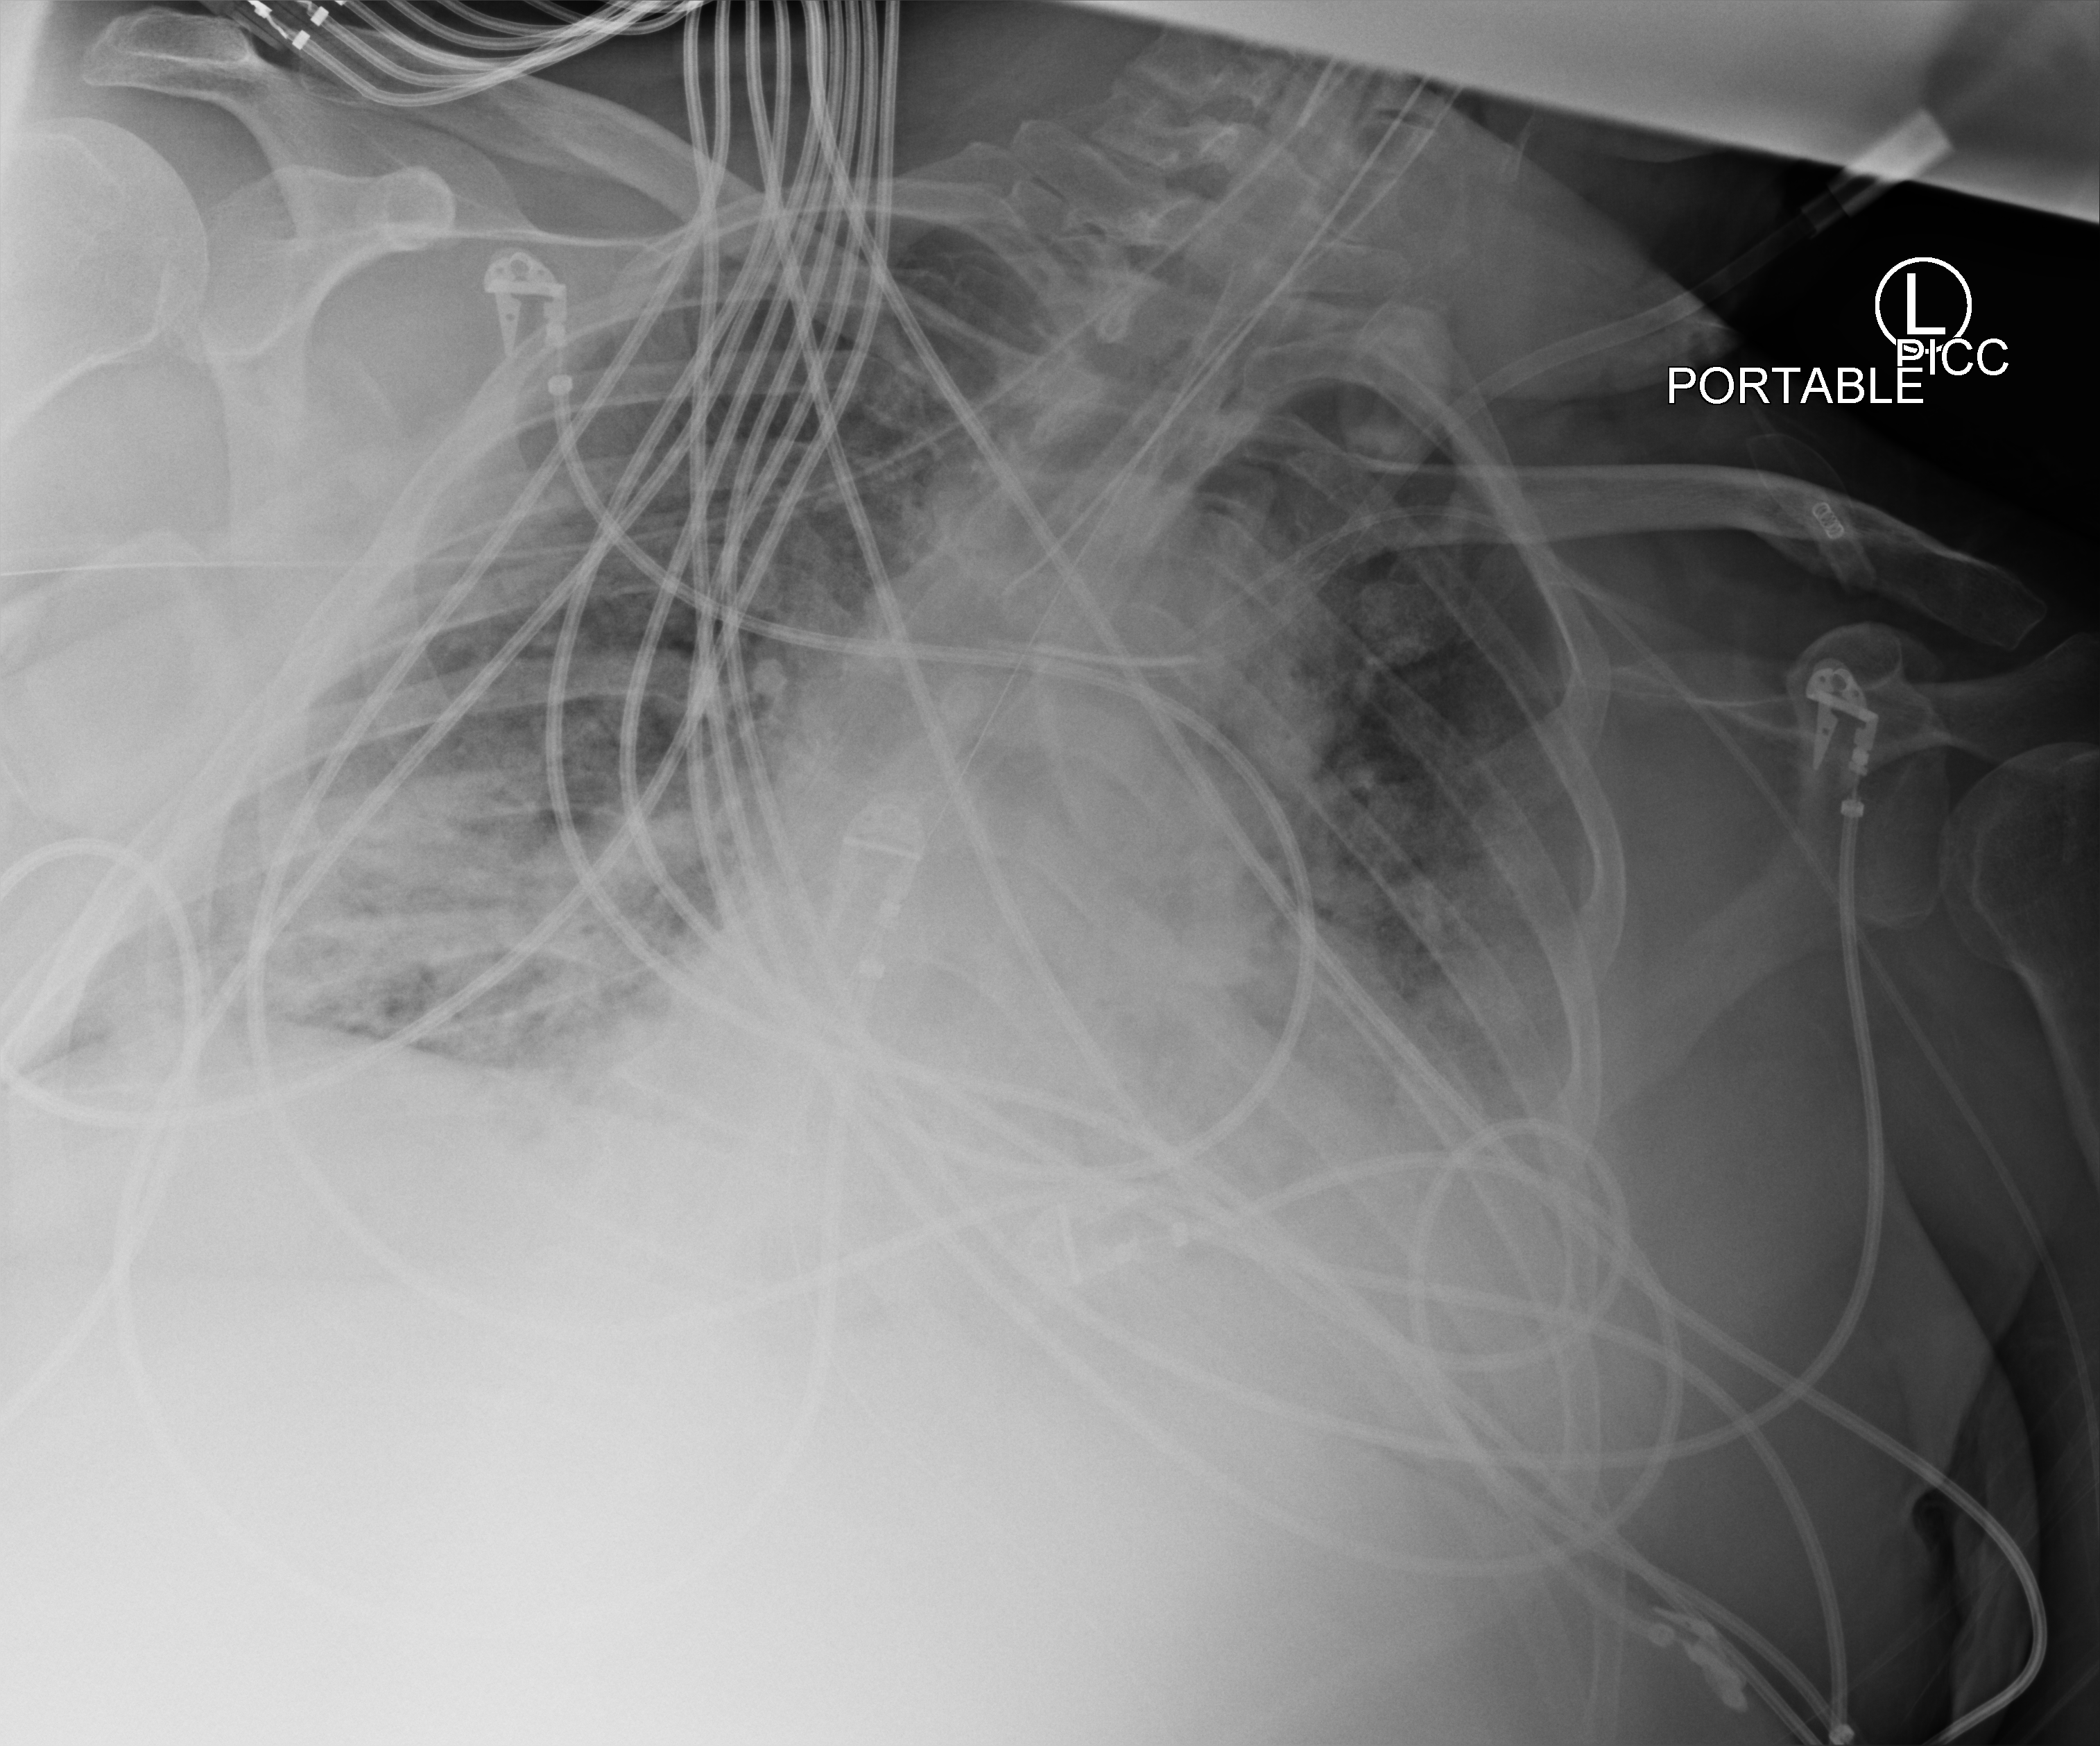
Chest X-ray (portable). Male patient hospitalised with COVID-19, age 18–59 years.
From the hospital-stay record, not from the radiograph (when in the stay this image was taken is not recorded): mechanically ventilated during this hospital stay: yes.